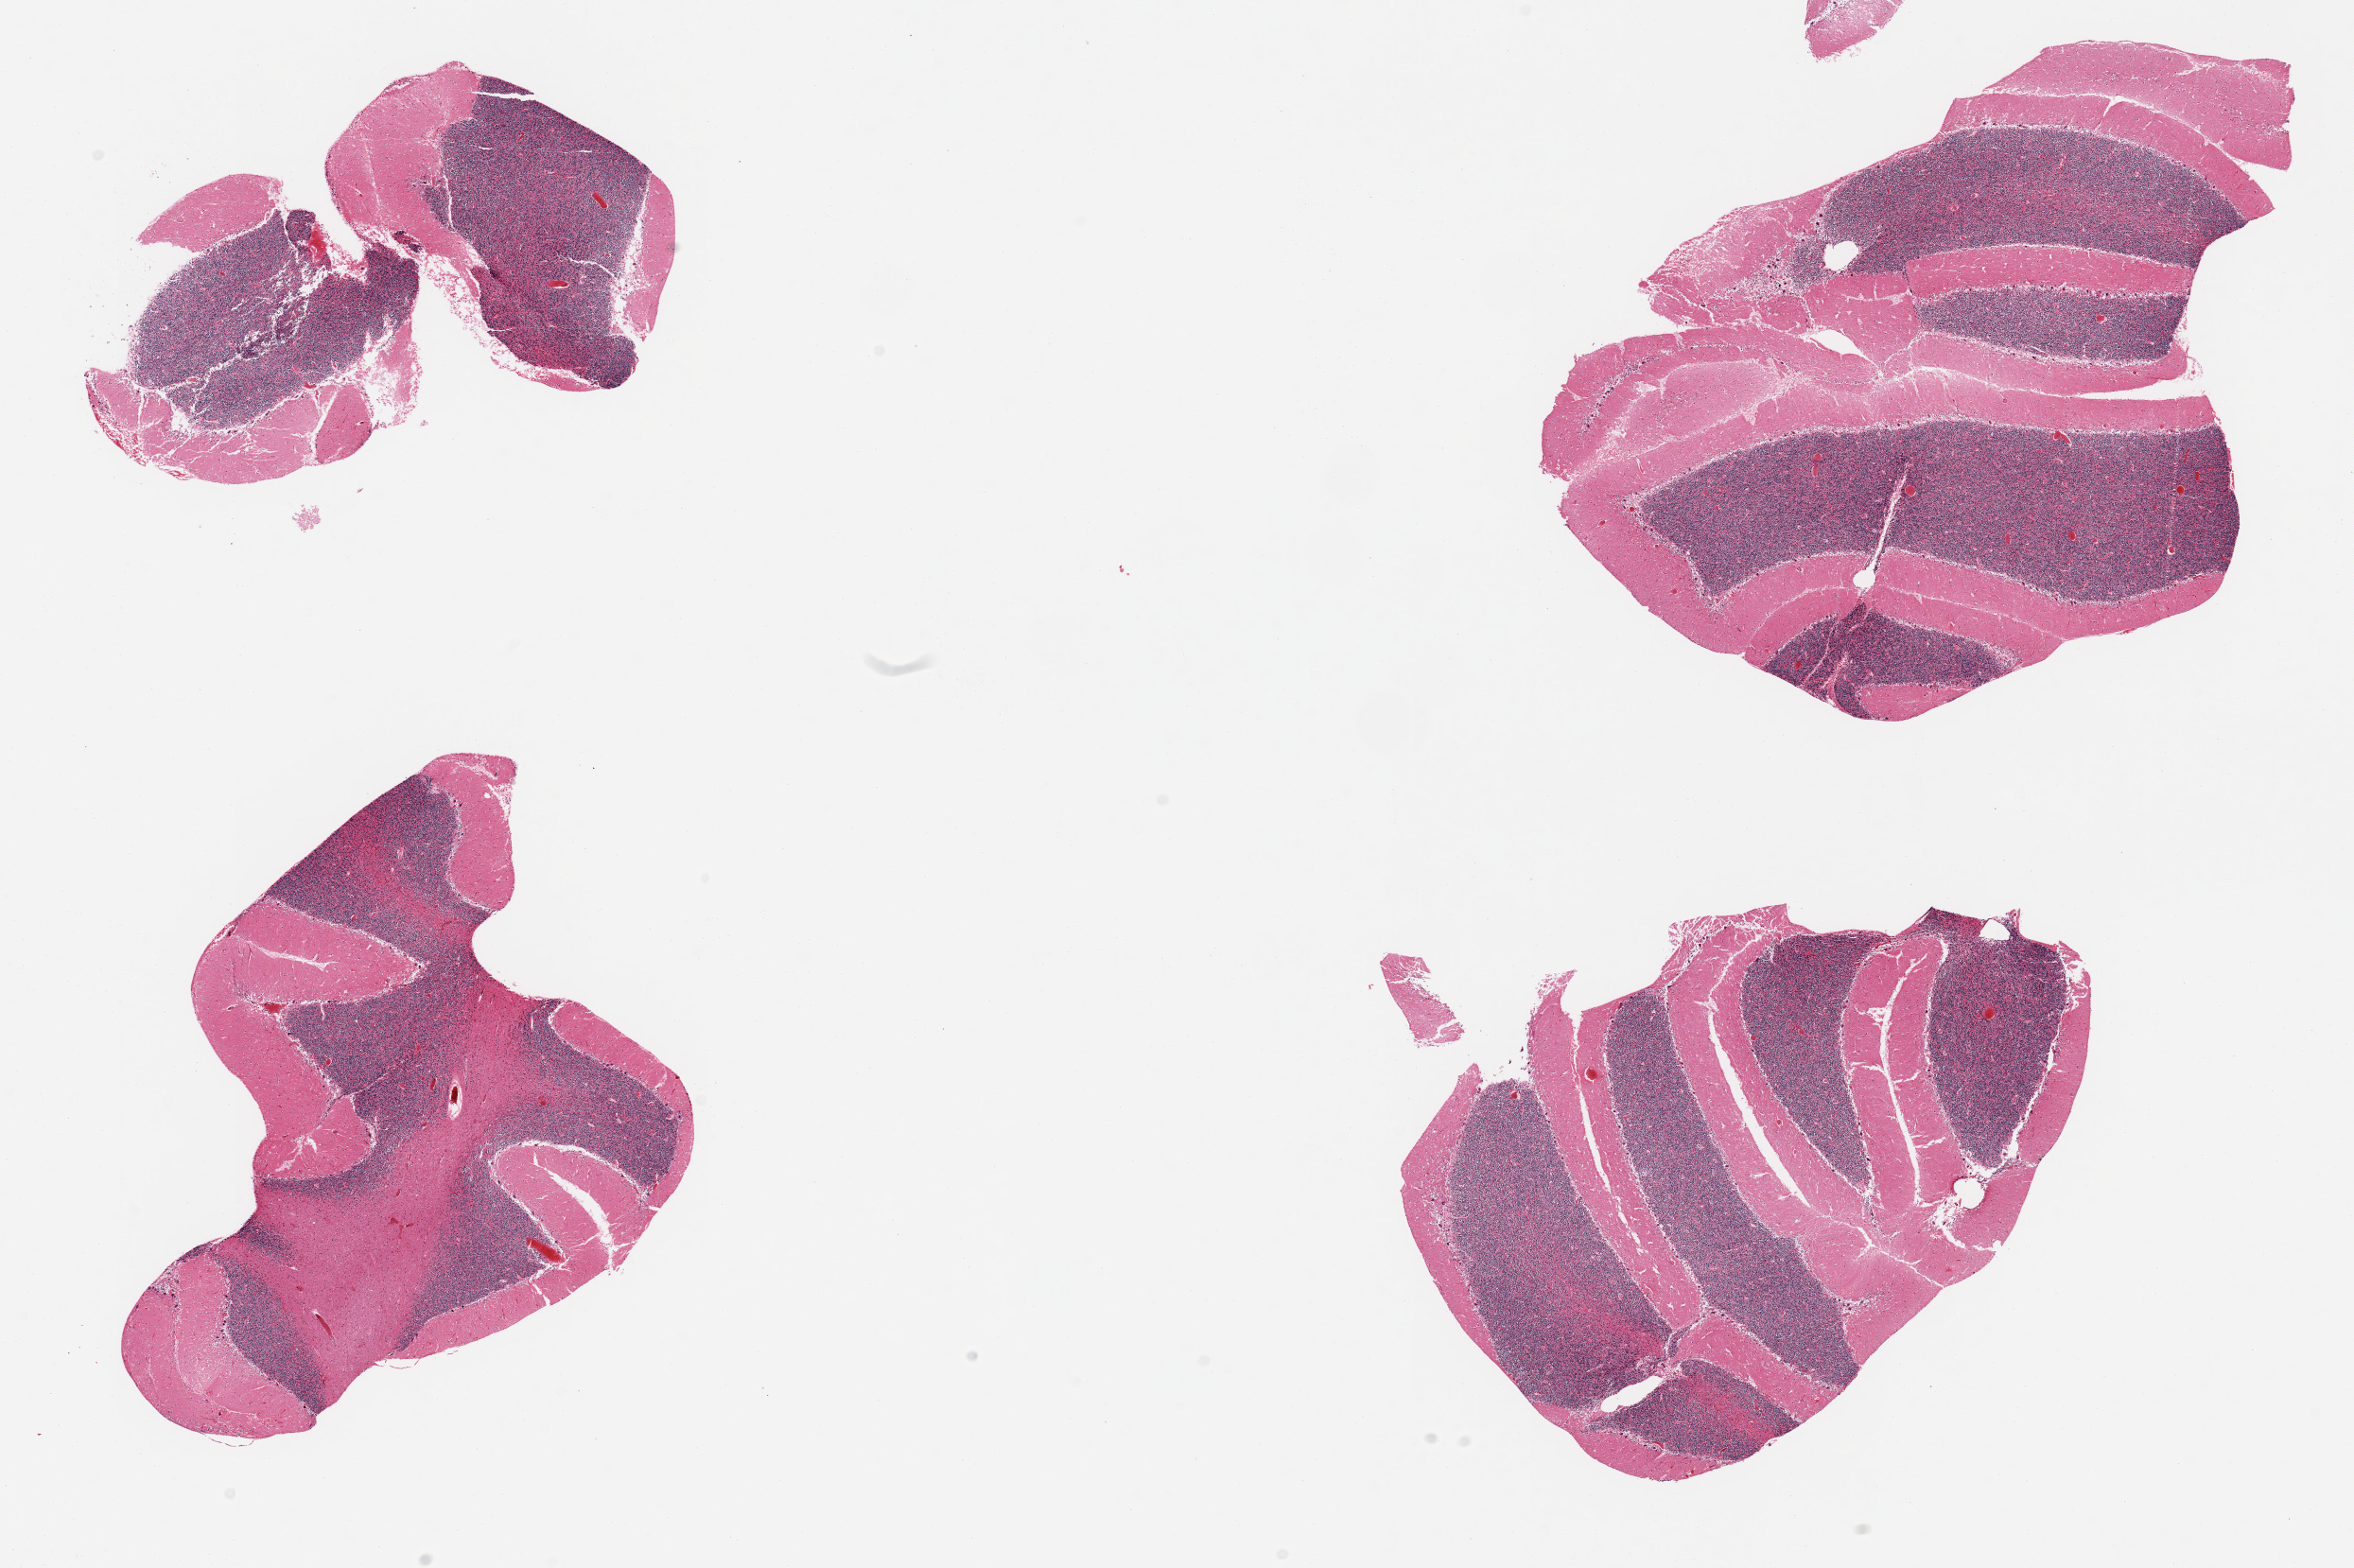
Digitized hematoxylin and eosin (H&E)-stained section, brightfield — shown as a low-resolution overview of the whole scanned area (about 19.7 x 13.1 mm), PAXgene-fixed, paraffin-embedded tissue, target tissue: cerebellum, tissue donor sample. Male donor.
Reviewer comment on this tissue sample: 4 pieces, no abnormalities.